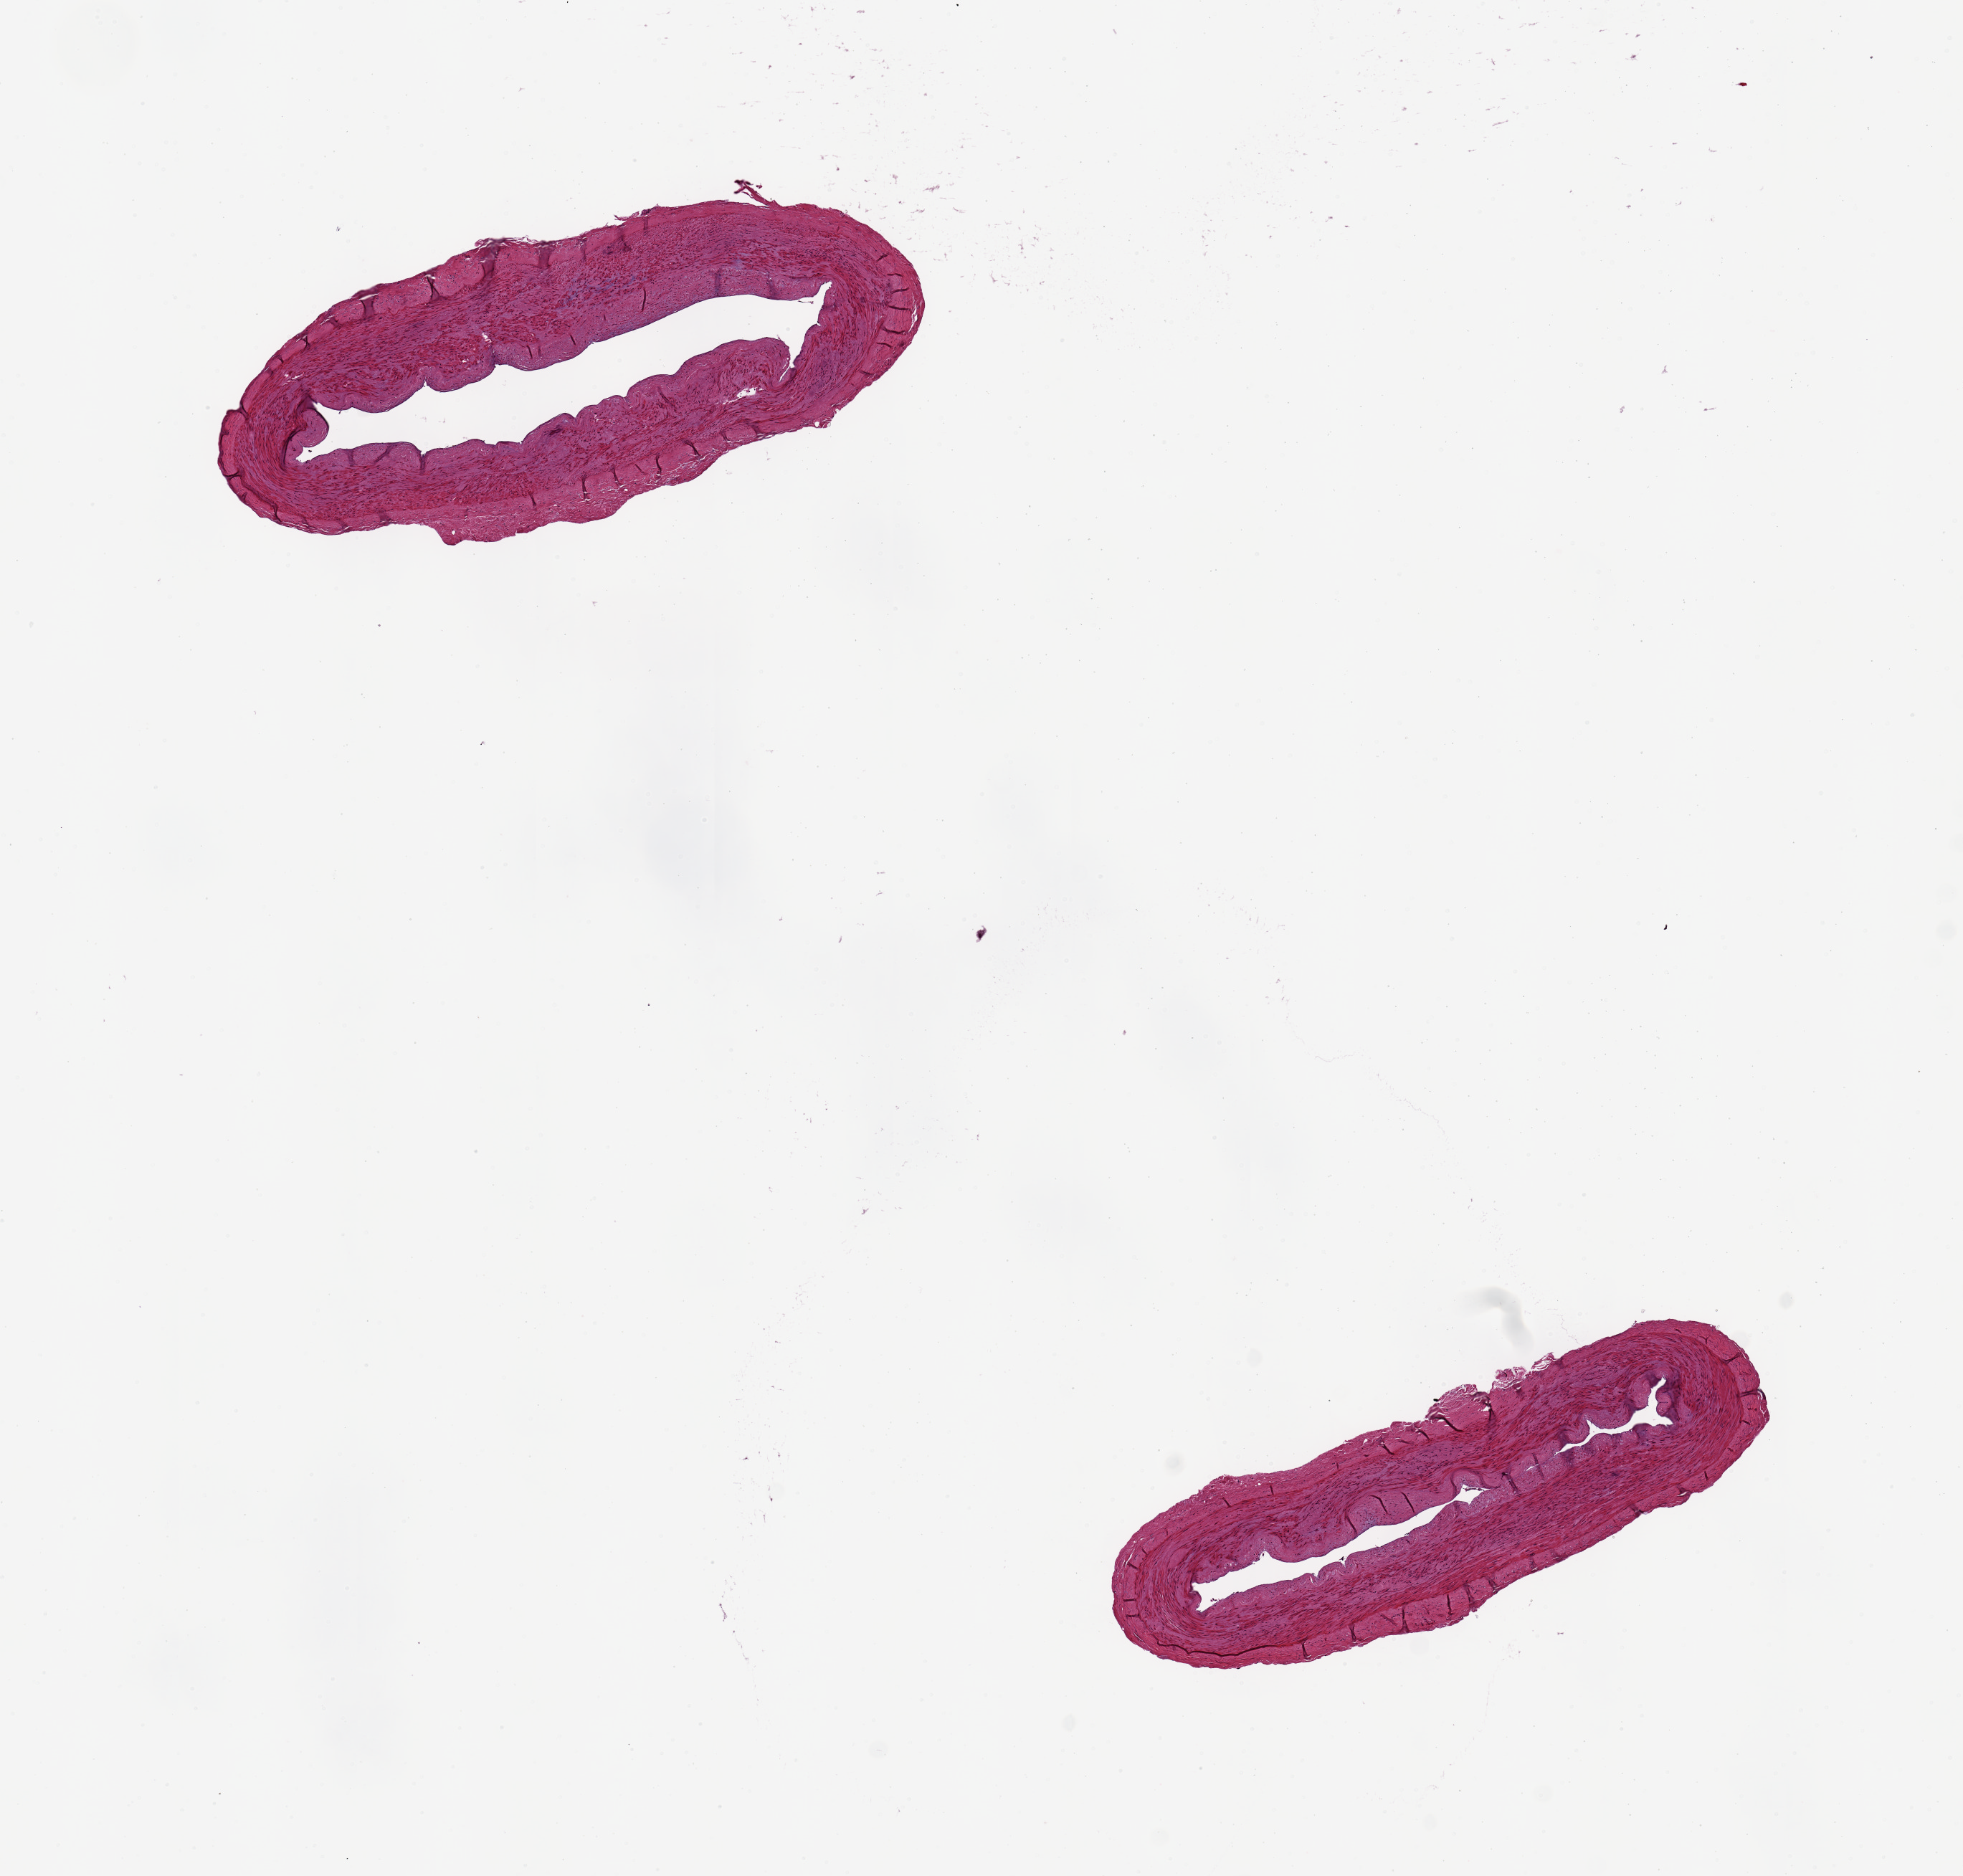
H&E whole-slide image, brightfield, whole scanned area (about 10.8 x 10.3 mm) shown as a low-resolution overview. PAXgene-fixed, paraffin-embedded tissue. Section of tibial artery (target tissue). Tissue donor sample.
• reviewer comment on this tissue sample: 2 pieces, 4x2 & 4x1mm; well trimmed